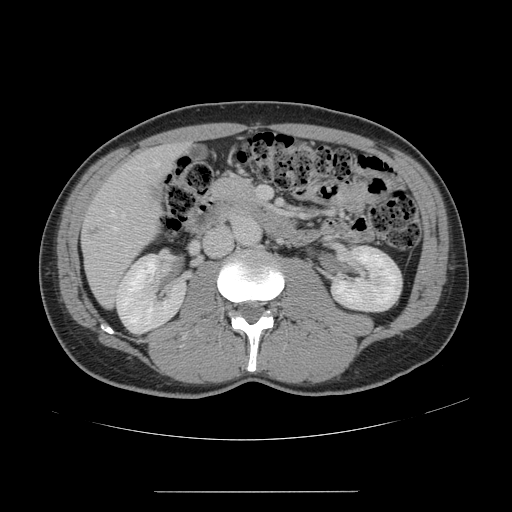
Contrast-enhanced abdominal CT, one axial slice; position 54 of 178 along the scan axis; intravenous contrast given; soft-tissue window (W 400 / L 40 HU); 512 × 512 image matrix, field of view 401 × 401 mm. Male patient, age 53 years. Case-level facts recorded for this patient, not image findings: diagnosis: colorectal cancer liver metastases, imaged before liver resection; multiple liver metastases: yes; largest metastasis: 2.4 cm; disease in both lobes: no.
Annotated regions visible in this slice (outlined manually by an expert reader):
- hepatic veins: box from (x=99, y=163) to (x=159, y=247) px
- liver: (x=83, y=146)–(x=181, y=305)
- portal vein (with intrahepatic branches): (x=259, y=186)–(x=267, y=199)
- liver metastasis: (x=150, y=183)–(x=160, y=201)
- liver metastasis: (x=90, y=228)–(x=100, y=236)